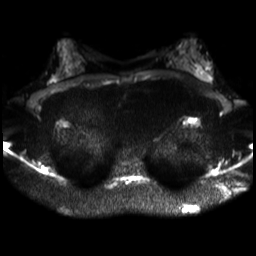
Breast MRI, one axial slice. Position 17 of 30 along the scan axis. Diffusion-weighted series; image 2 of 4 stored at this slice position (different b-values; order by instance number). 3 T. 4 mm slice thickness. 256 × 256 image matrix, field of view 320 × 320 mm. Female patient.
Annotated regions visible in this slice (manually delineated by an expert):
- tumour on diffusion-weighted imaging: bounding box (x1, y1, x2, y2) in pixels: (198, 68, 206, 80)